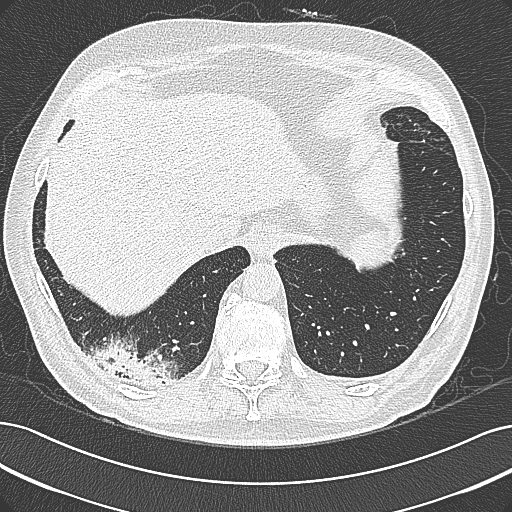
Low-dose screening chest CT, axial slice; first (baseline) screen; lung window (W 1500 / L -600 HU); lung (sharp) reconstruction kernel (B80f); 120 kVp. Male, age 68 years at enrolment. Former smoker at enrolment.
Expert-annotated lung lesion, bounding box (x1, y1, x2, y2) in pixels: (95, 339, 189, 400). No non-calcified nodule or mass ≥4 mm was recorded by the screening reader at this exam. Official screen result: negative screen, significant abnormalities not suspicious for lung cancer. Lung cancer was diagnosed 154 days after this screen: mucinous adenocarcinoma, right lower lobe, well differentiated (G1), stage IB (AJCC 6th edition), 50 mm at pathology.